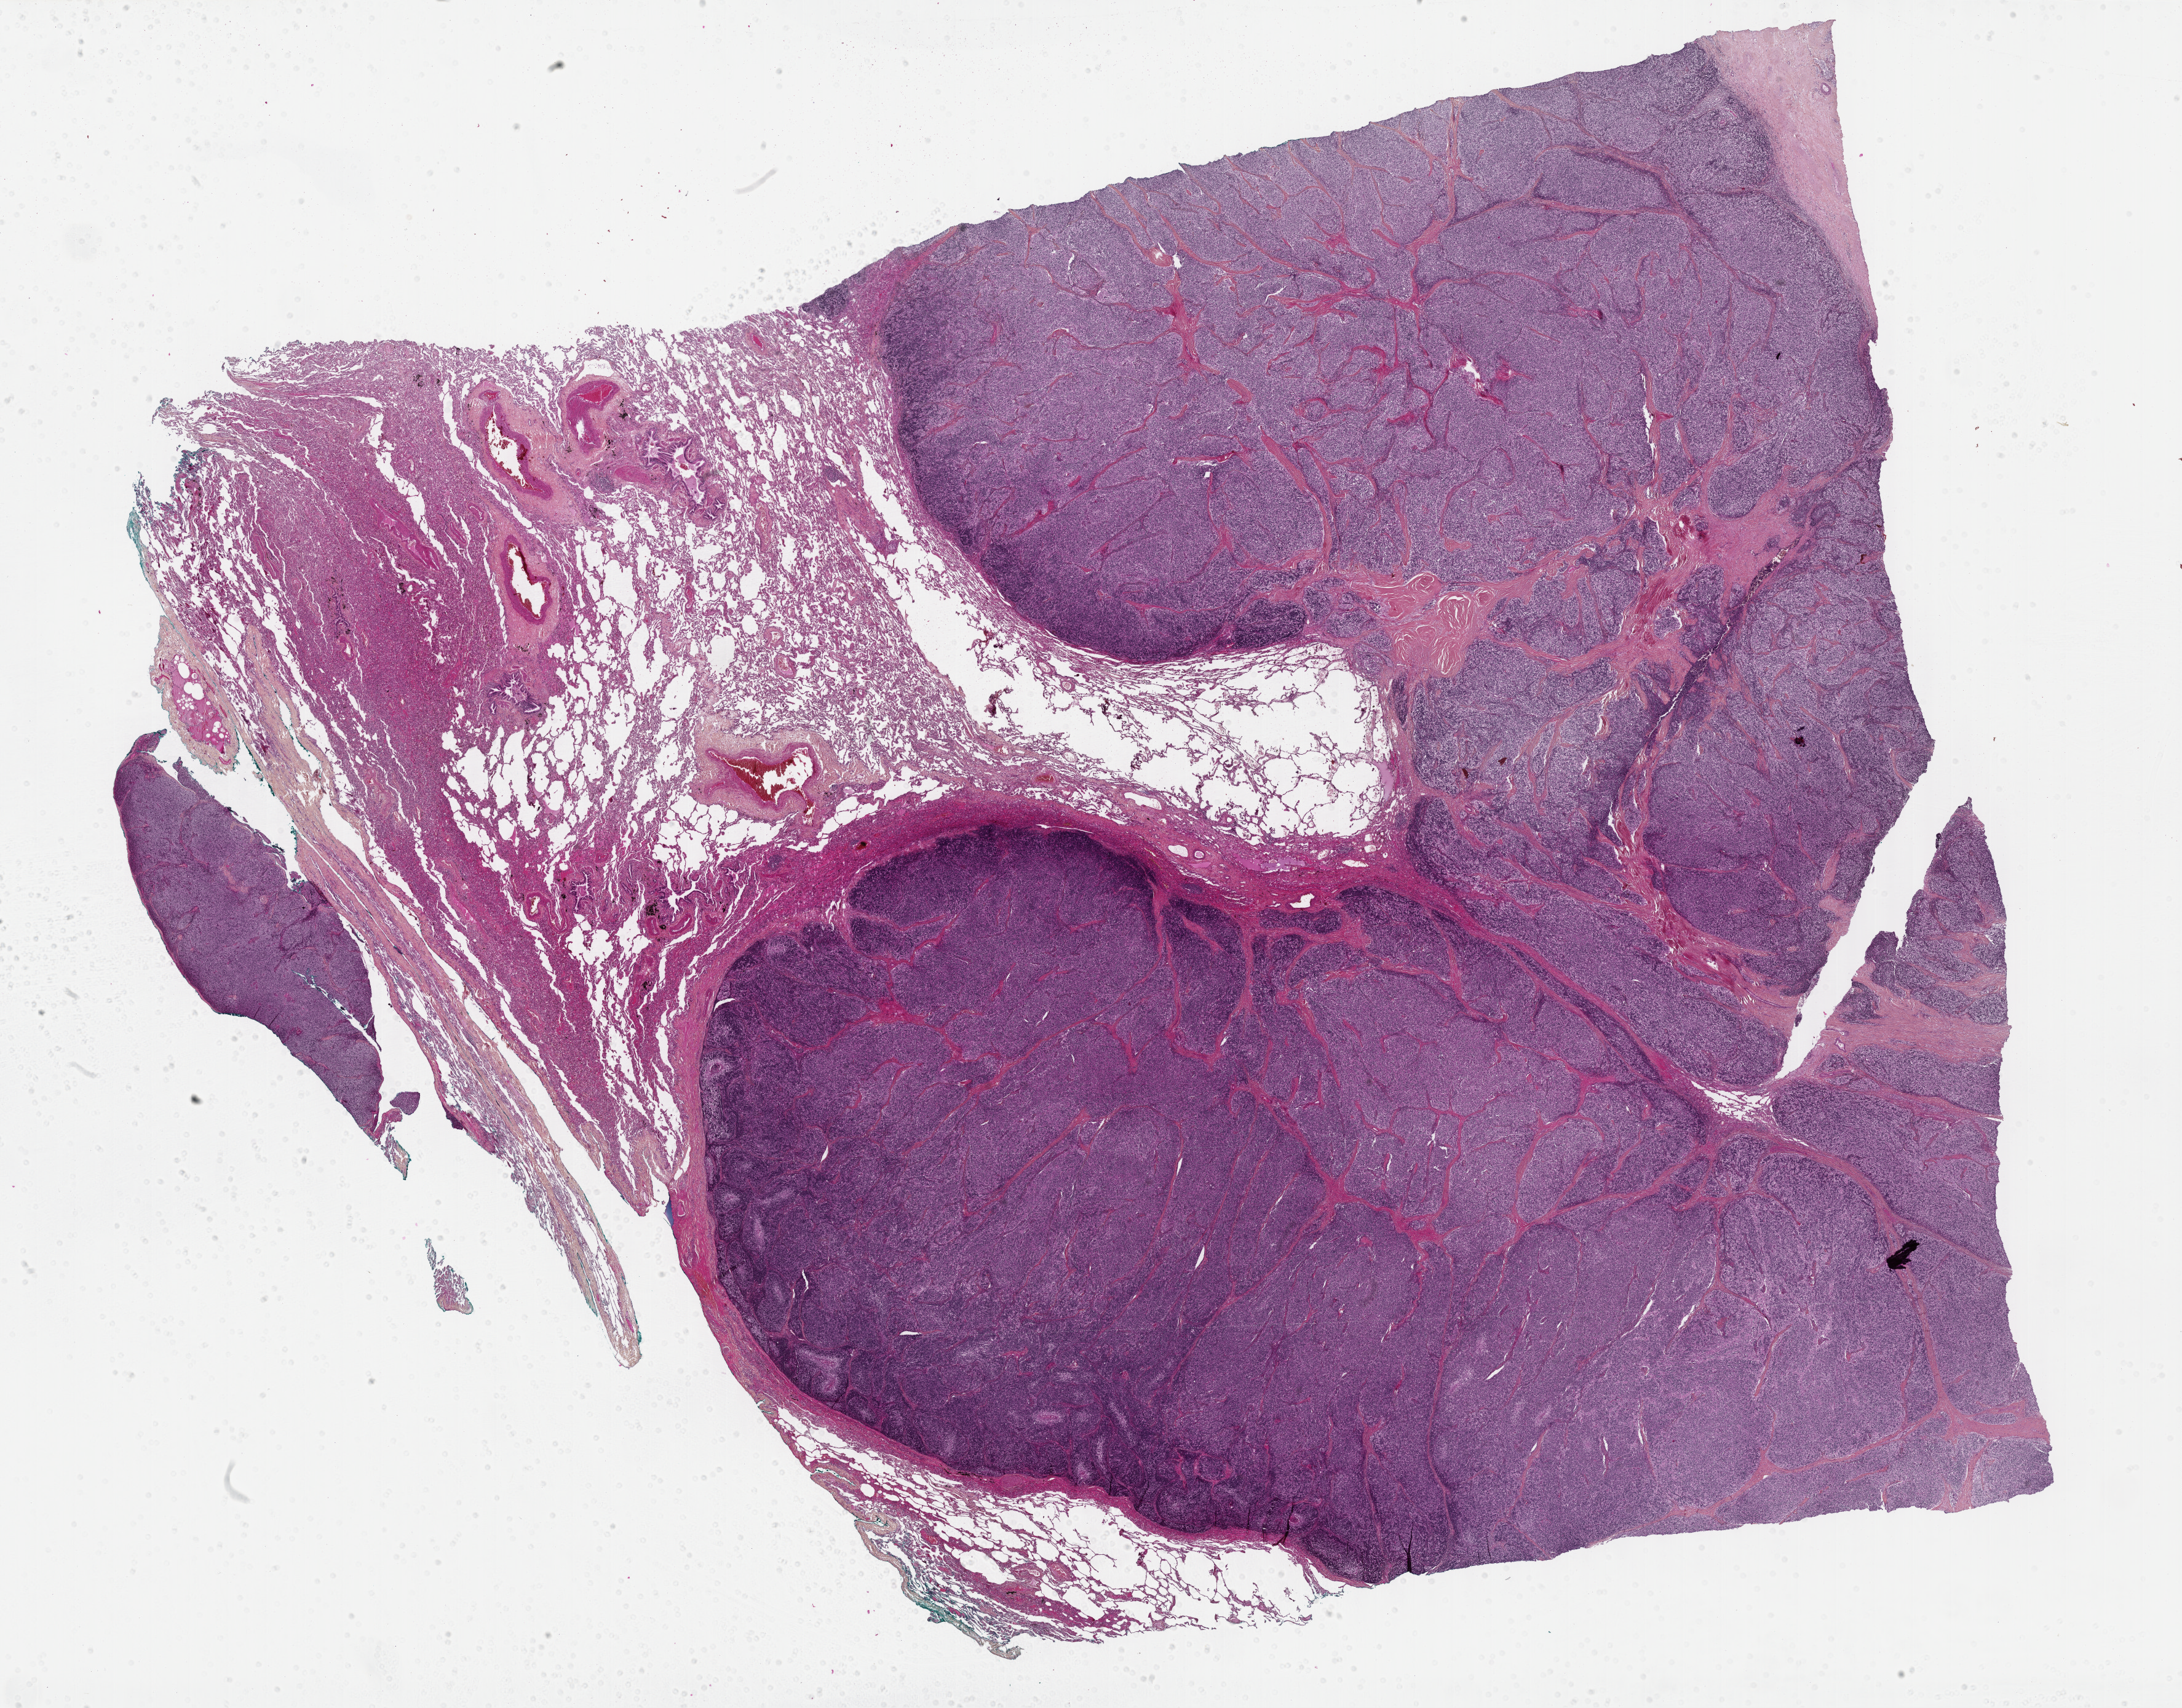
Whole-slide histology image, Hematoxylin and eosin (H&E) stained — a low-resolution overview of the entire scanned area, about 28.7 x 22.5 mm. FFPE section. Thymus, primary tumour sample. Female, age 53 years at initial diagnosis.
Diagnosis: Thymoma, type B2, malignant.